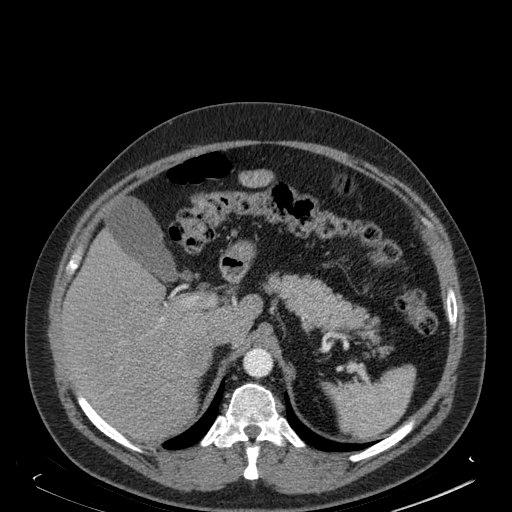
Contrast-enhanced abdominal CT, one axial slice; position 129 of 181 along the scan axis; soft-tissue window (W 400 / L 40 HU); 1.5 mm slice thickness; 512 × 512 image matrix, field of view 405 × 405 mm. Male patient. From the clinical record (not read from this slice): diagnosis: adrenocortical carcinoma; tumour side: right adrenal; tumour size at pathology: 7.5 cm; Ki-67 index: 25 %; stage (as recorded): 4.
Outlined on this slice (semi-automatically segmented with operator editing):
- mass: bounding box [x1, y1, x2, y2] px = [186, 338, 206, 372]